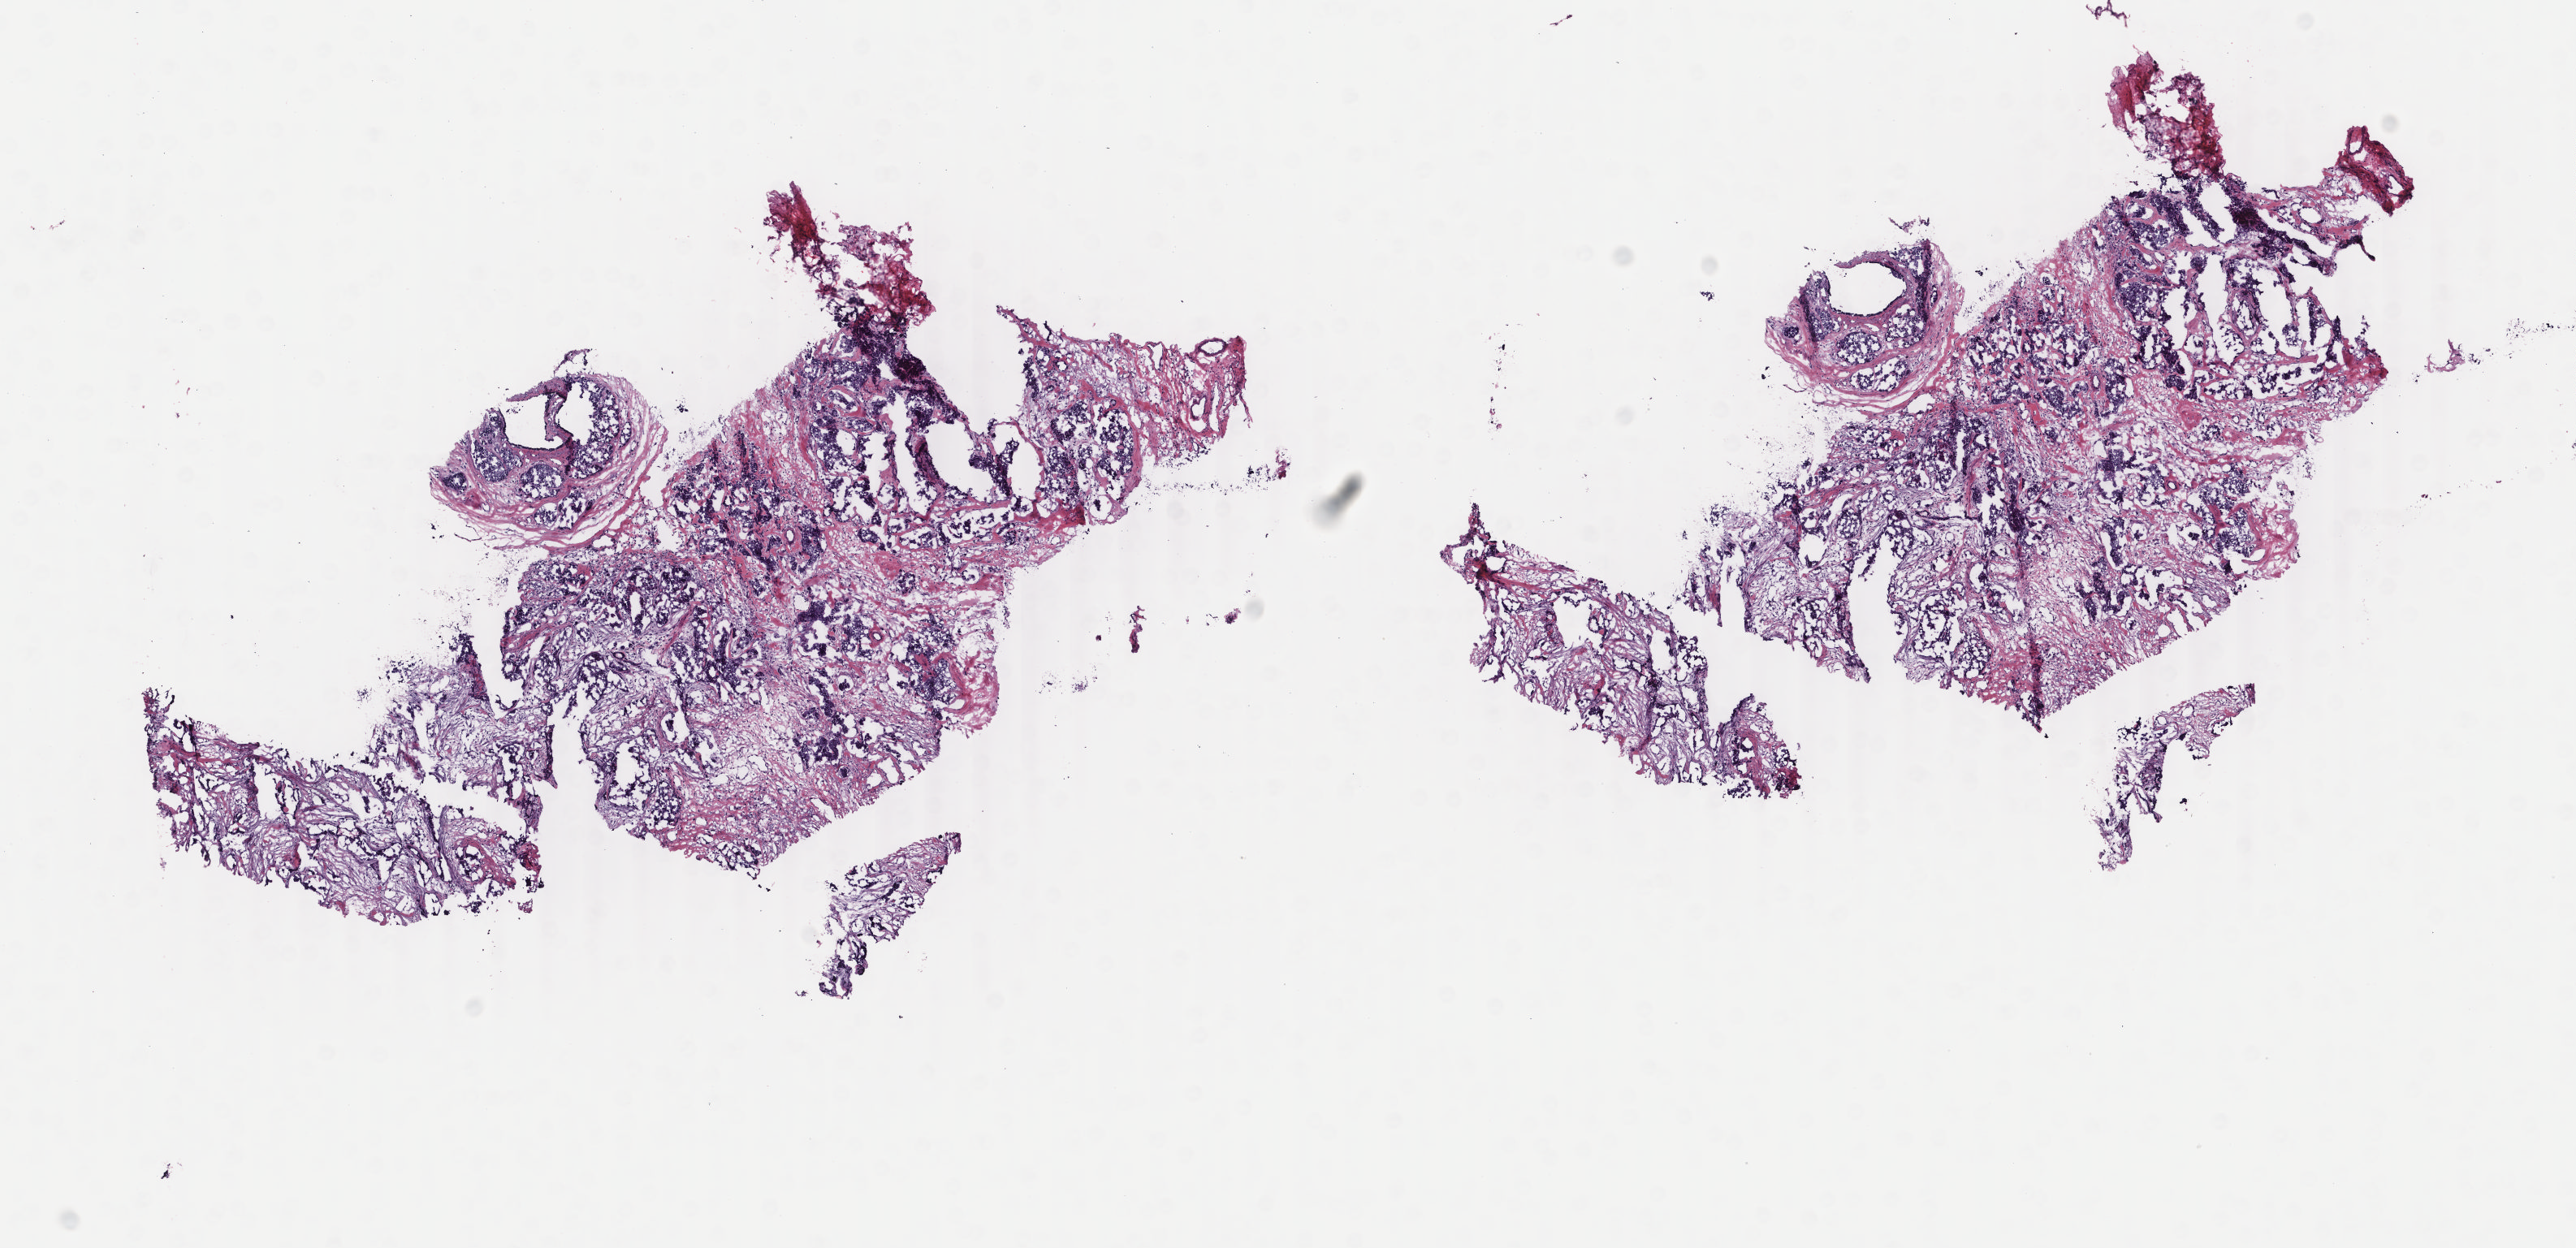
Whole-slide histology image, H&E-stained, whole scanned area (about 12.6 x 6.1 mm) shown as a low-resolution overview; frozen section from the bottom of the tissue portion; primary tumour sample from the breast. Female, age 67 years at initial diagnosis. Composition of this section per pathologist review: tumour cells 75%, tumour nuclei 75%, normal cells 0%, stromal cells 25%, necrosis 0%. Infiltration values recorded for this section: lymphocyte infiltration 3%, monocyte infiltration 1%, neutrophil infiltration 1%.
Histologic diagnosis: Infiltrating duct carcinoma, NOS. AJCC pathologic stage: IIB (4th edition).